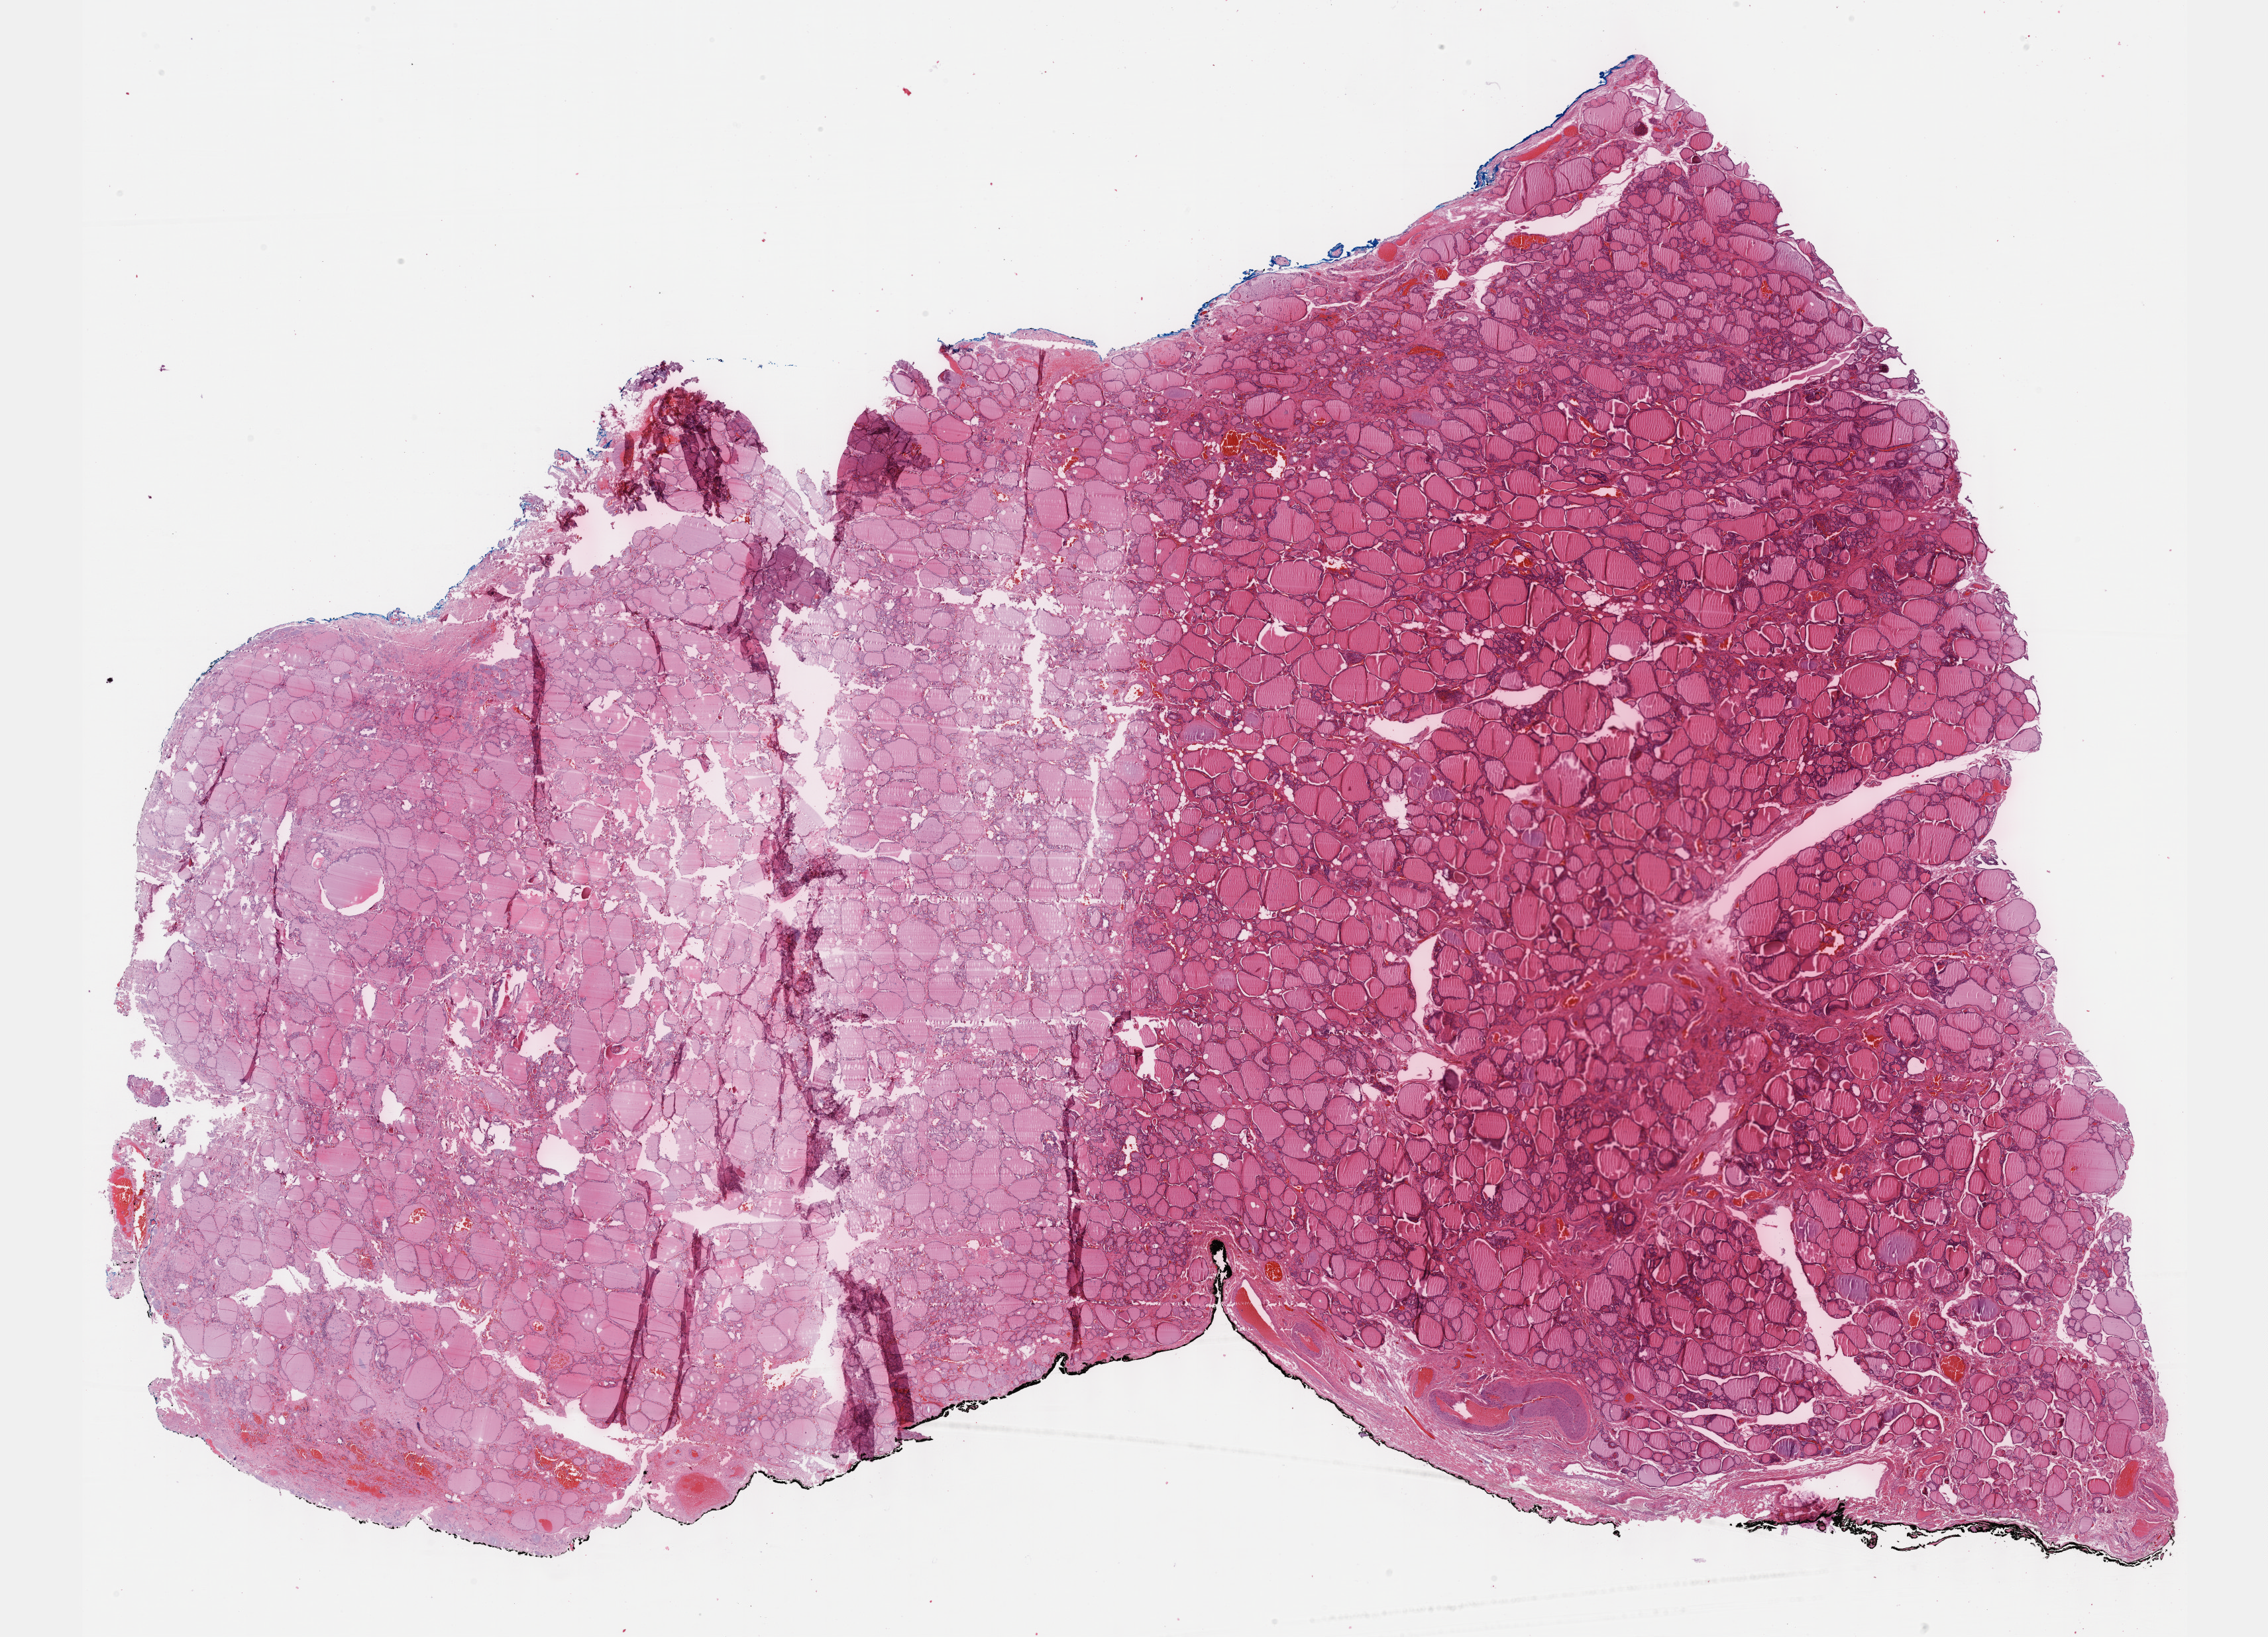
Digitized H&E tissue section (whole slide) — shown as a low-resolution overview of the whole scanned area (about 27.7 x 20.0 mm, acquisition: 40x scan); formalin-fixed paraffin-embedded (FFPE) diagnostic section; primary tumour sample from the thyroid. Male patient; age at initial diagnosis 74 years.
Pathologic diagnosis: Papillary carcinoma, follicular variant.